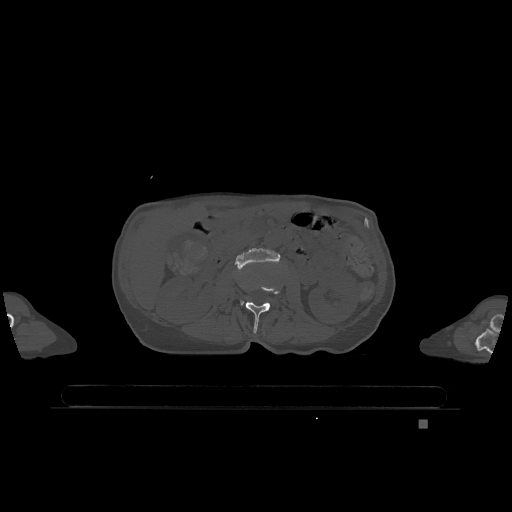
CT including the spine, one axial slice; slice 398 of 1317 in the series (ordered by position); bone window (W 1800 / L 400 HU); 0.5 mm slice thickness; 512 × 512 image matrix. Female patient, age 74 years. Case-level facts recorded for this patient, not image findings: primary cancer: lung; vertebrae with lytic lesions (as recorded): T1, T4, T5, T6, L4, L5.
Annotated regions visible in this slice (semi-automatic segmentation, software-assisted and operator-edited):
- L2 vertebra: box from (x=246, y=286) to (x=279, y=333) px
- L3 vertebra: (x=235, y=248)–(x=280, y=305)